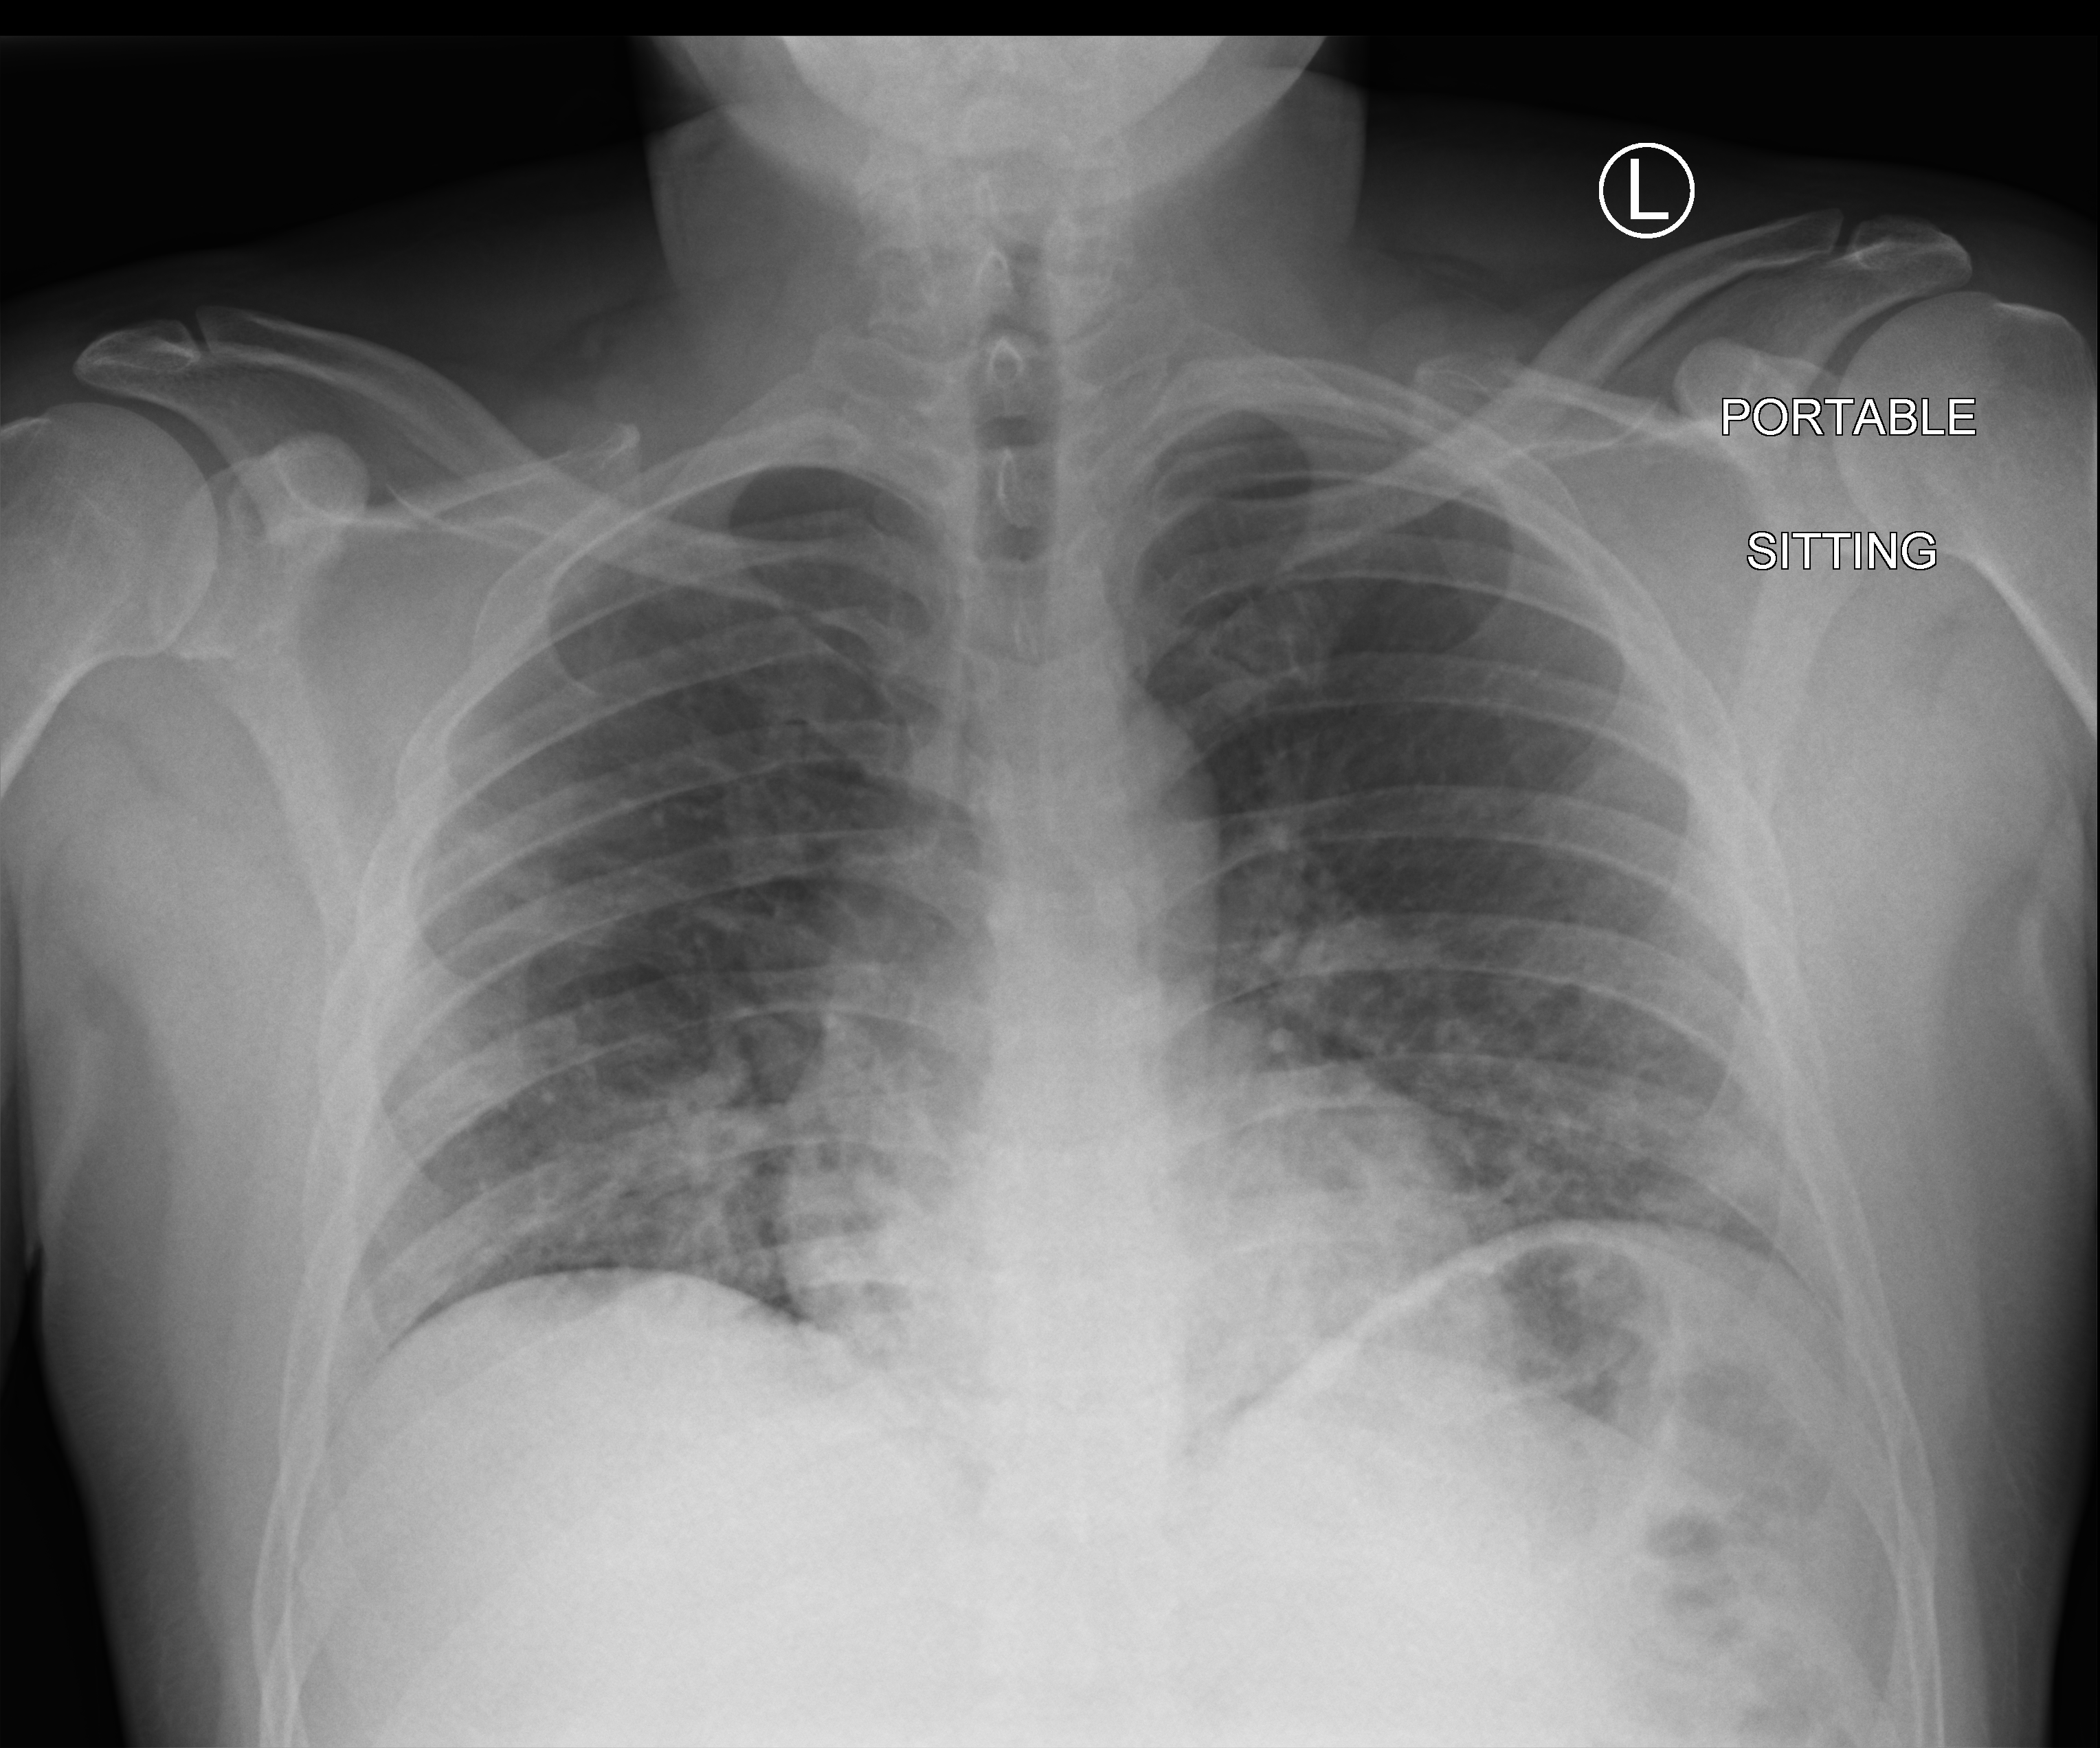
Bedside chest radiograph (computed radiography); anteroposterior (AP) projection. Patient hospitalised with COVID-19; male, aged 18–59 years.
From the hospital-stay record, not from the radiograph (when in the stay this image was taken is not recorded):
- mechanically ventilated during this hospital stay: no
- chronic kidney disease (admission record): no